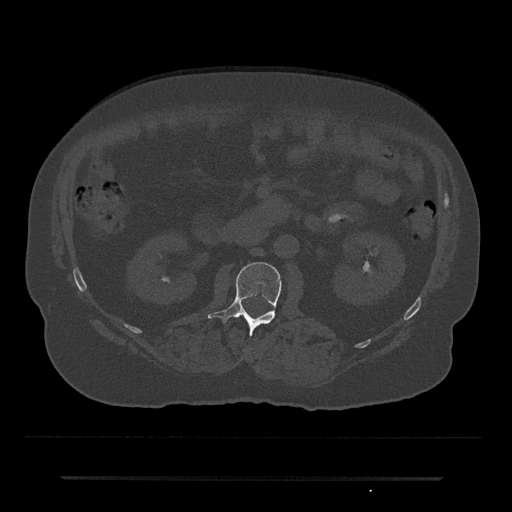
CT including the spine, one axial slice; slice 13 of 797 in the series (ordered by position); reconstruction kernel Br40s/3; bone window (W 1800 / L 400 HU); 0.5 mm slice thickness; 512 × 512 image matrix, field of view 437 × 437 mm. Male patient, age 69 years. From the clinical record (not read from this slice): primary cancer: prostate.
Annotated regions visible in this slice (semi-automatic segmentation, software-assisted and operator-edited):
- L2 vertebra: bounding box (x1, y1, x2, y2) in pixels: (208, 262, 282, 336)